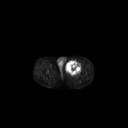
FDG PET of an extremity soft-tissue mass (from a PET/CT study), one axial slice. Position 254 of 267 along the scan axis. 128 × 128 image matrix, field of view 700 × 700 mm. Male patient, age 63 years. From the clinical record (not read from this slice): histological type: pleiomorphic liposarcoma; grade: high; site of the primary tumour: left thigh.
Annotated regions visible in this slice (expert contour drawn on MRI and transferred to this co-registered scan by the dataset authors):
- gross tumour volume including surrounding oedema: box from (x=66, y=60) to (x=81, y=74) px
- gross tumour volume (mass): (x=66, y=61)–(x=81, y=74)